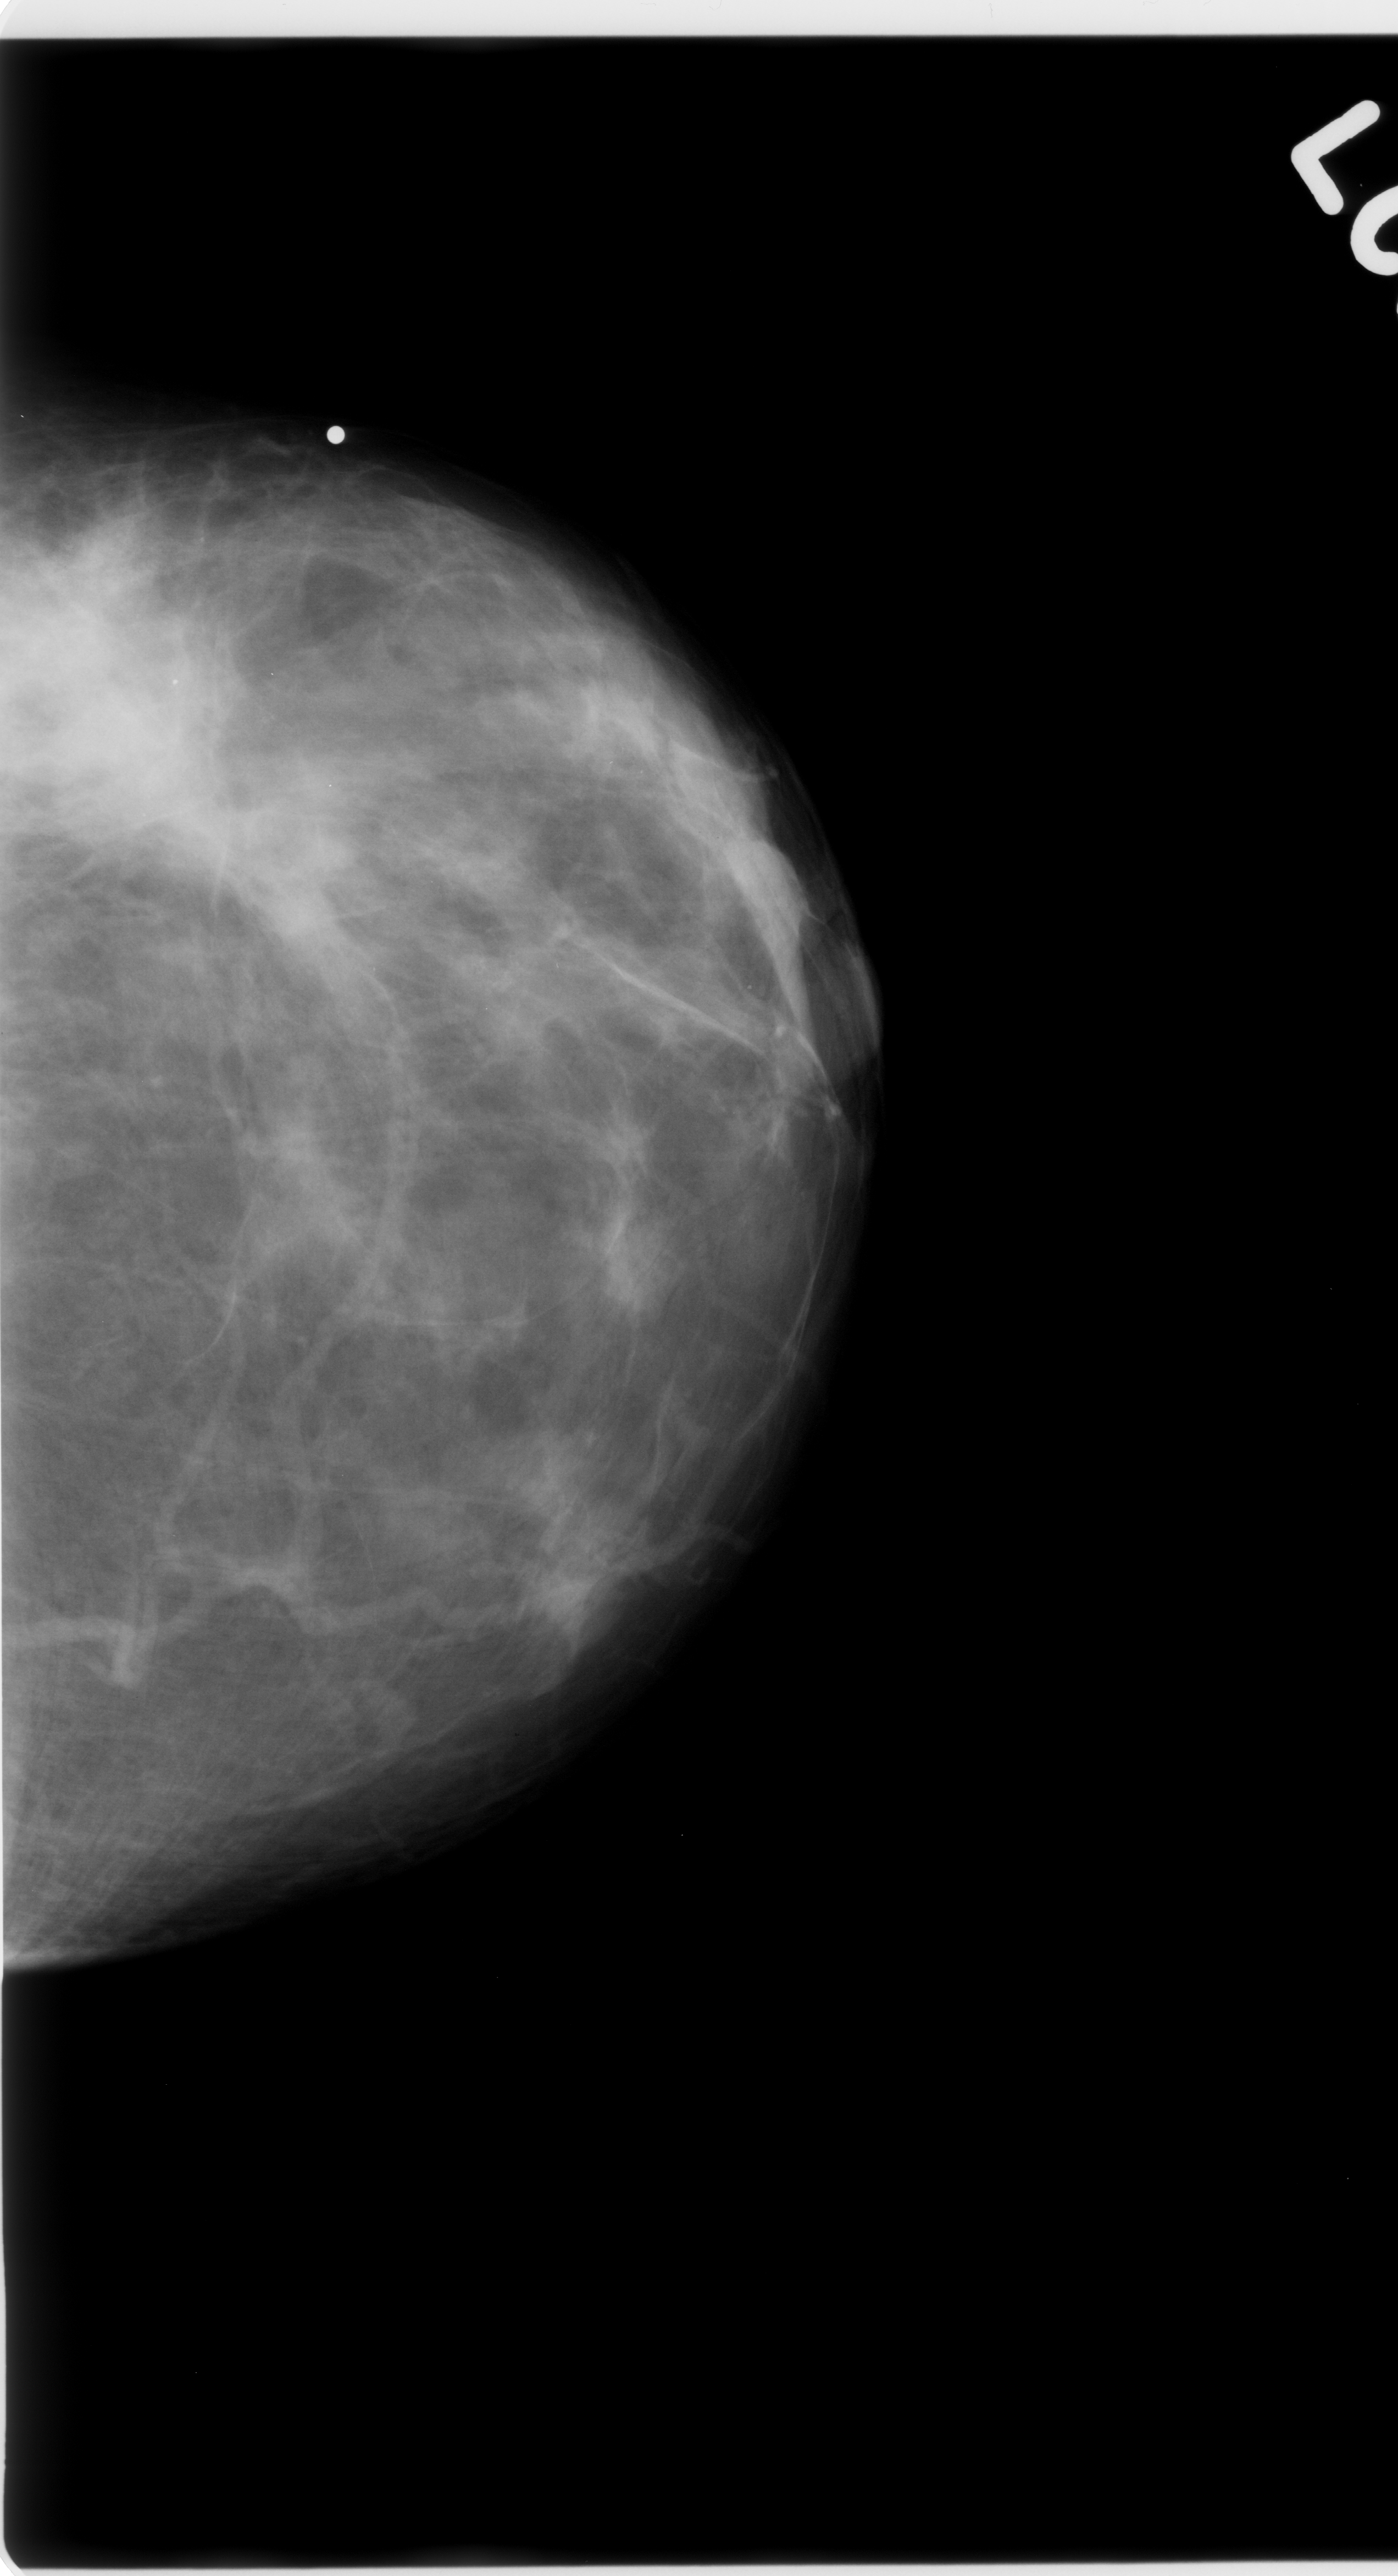
Mammogram (digitized film). Left breast. Craniocaudal (CC) view. Breast composition: scattered fibroglandular densities (BI-RADS density category 2 of 4). 1398 × 2576 image matrix.
Expert-marked regions of interest on this film, with their recorded descriptors:
- mass, shape irregular, margins ill defined; BI-RADS assessment category 5; pathology (as recorded): malignant: box from (x=11, y=583) to (x=248, y=868) px